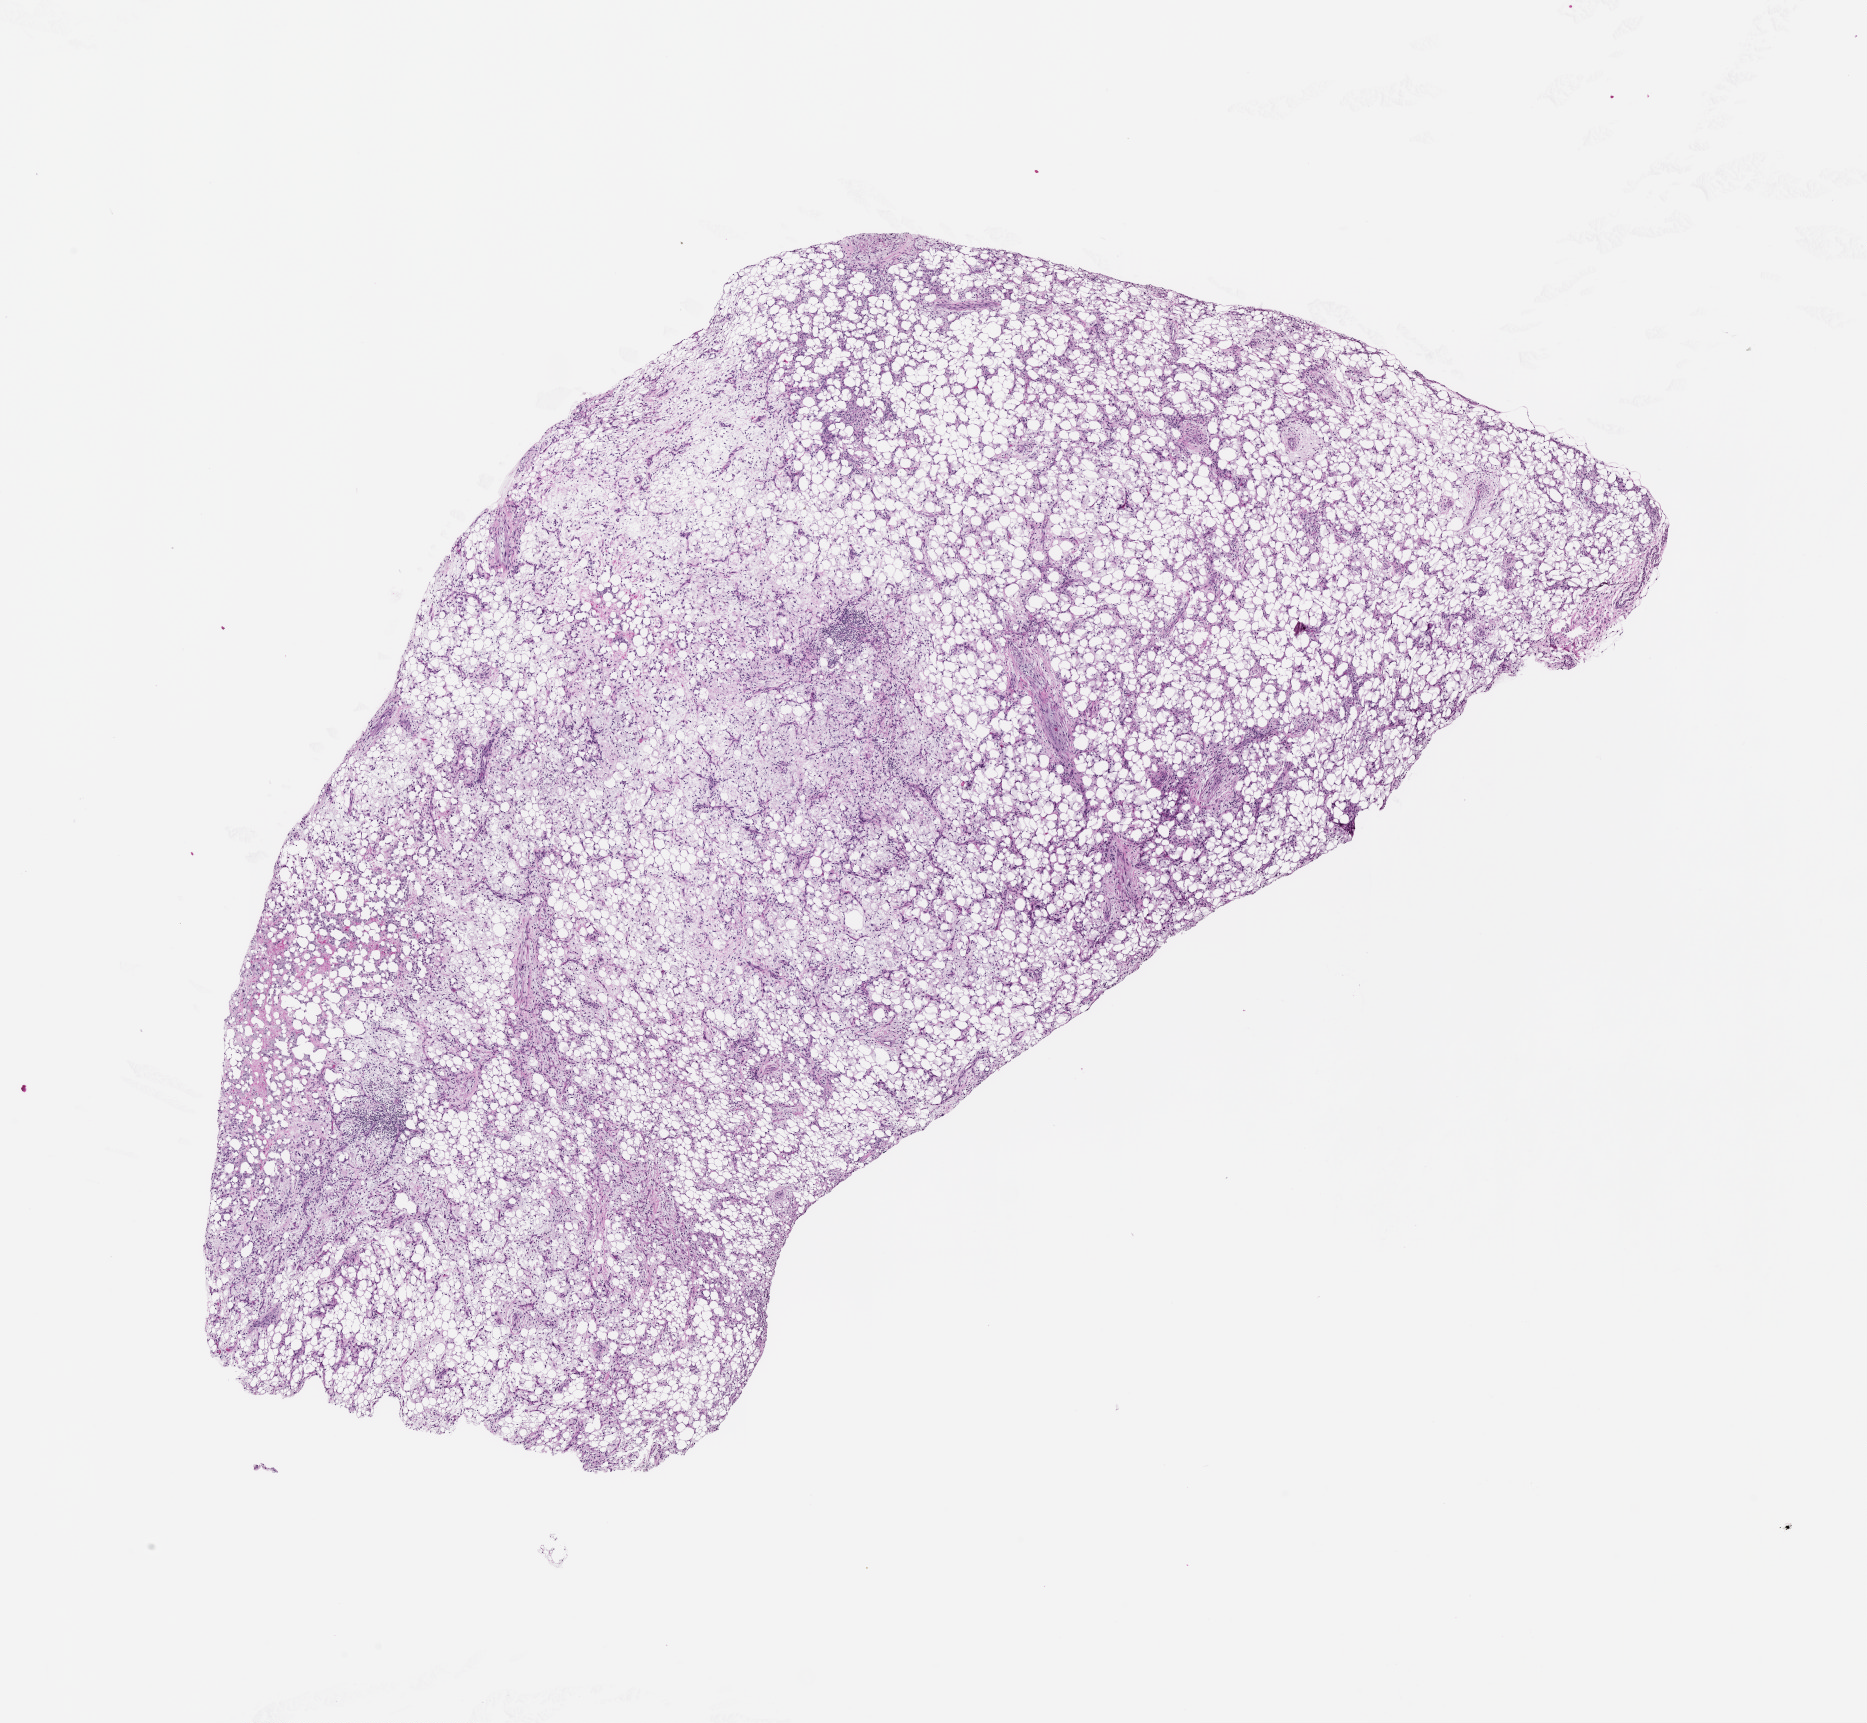
Digitized Hematoxylin and eosin (H&E) stained tissue section (whole slide) — shown as a low-resolution overview of the whole scanned area (about 15.0 x 13.9 mm).
Patient diagnosis (cohort enrolment): sarcoma (site not recorded at cohort level).